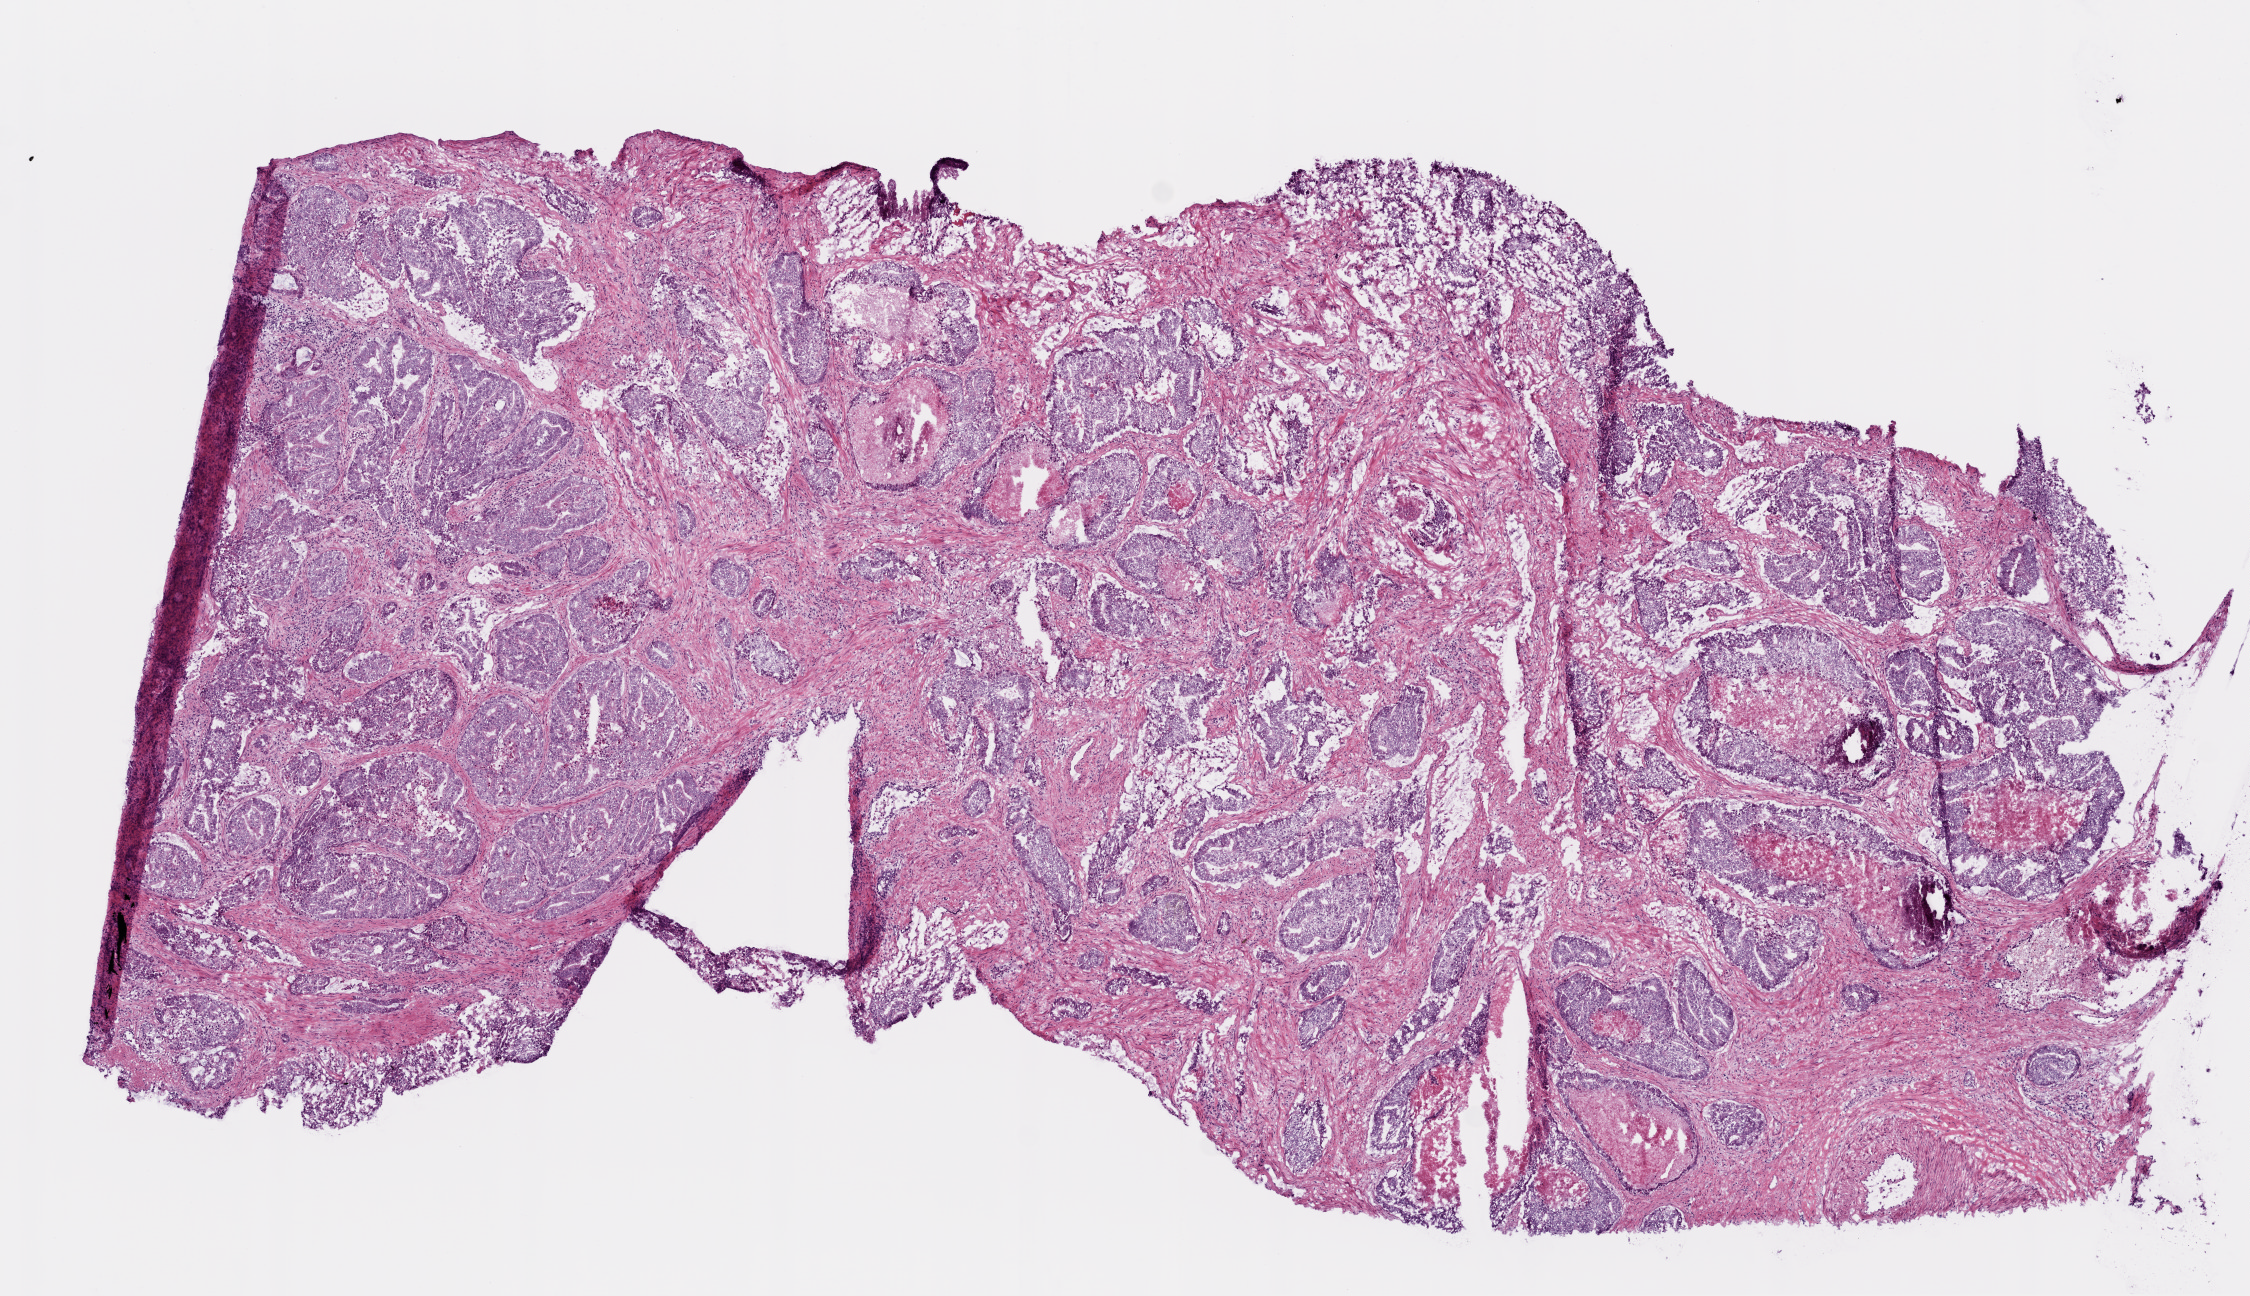
Digitized H&E tissue section (whole slide) — whole scanned area (about 9.0 x 5.2 mm, from a 20x scan) shown as a low-resolution overview, frozen section, primary tumour sample from the prostate. Male, age 48 years at initial diagnosis. Gleason score: 9 (5+4). Pathologist review of this section (percent, as recorded): tumour cells 55%, tumour nuclei 60%, normal cells 20%, stromal cells 10%, necrosis 15%. Inflammatory infiltration, as recorded: lymphocyte infiltration 2%, monocyte infiltration 3%, neutrophil infiltration 0%.
Laterality: bilateral. Pathologic diagnosis: Acinar cell carcinoma. Lymph nodes positive (case pathology): 0 of 8 examined.